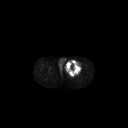
FDG PET of an extremity soft-tissue mass (from a PET/CT study), one axial slice; position 251 of 267 along the scan axis; 3.27 mm slice thickness; 128 × 128 image matrix, field of view 700 × 700 mm. Male patient, age 63 years. From the clinical record (not read from this slice): histological type: pleiomorphic liposarcoma; grade: high; site of the primary tumour: left thigh.
Outlined on this slice (expert contour drawn on MRI and transferred to this co-registered scan by the dataset authors):
- gross tumour volume including surrounding oedema: bounding box <65,60,82,75> (left, top, right, bottom; pixels)
- gross tumour volume (mass): <65,60,81,75>